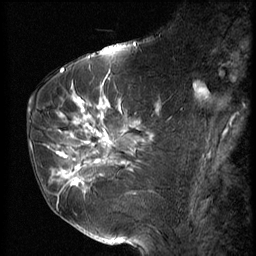
Breast MRI (dynamic contrast-enhanced), one sagittal slice; 3 images stored at this slice position (order not interpretable as contrast timing); 1.5 T; TE 4.2 ms, TR 9 ms; 256 × 256 image matrix, field of view 180 × 180 mm. Female patient, age 61 years. Case-level facts recorded for this patient, not image findings: setting: breast cancer imaged before/during neoadjuvant chemotherapy; receptor status: HR-positive, HER2-negative.
Annotated regions visible in this slice (semi-automatically segmented with operator editing):
- analysis volume of interest (the breast-tissue region the enhancement analysis was run in; not a lesion): bounding box (x1, y1, x2, y2) in pixels: (47, 89, 153, 191)
- tumour enhancement mask (voxels above the 140 % enhancement threshold inside the analysis volume of interest): (49, 97, 140, 188)